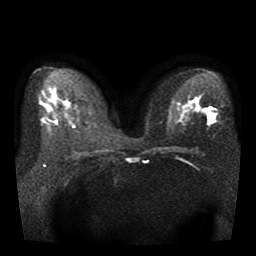
Breast MRI, one axial slice; position 21 of 41 along the scan axis; diffusion-weighted series; image 2 of 4 stored at this slice position (different b-values; order by instance number); 1.5 T; 256 × 256 image matrix. Female patient.
Annotated regions visible in this slice (manually delineated by an expert):
- tumour on diffusion-weighted imaging: bounding box (x1, y1, x2, y2) in pixels: (206, 109, 215, 120)